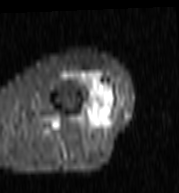
MRI of an extremity soft-tissue mass, one axial slice; position 30 of 103 along the scan axis; STIR; MR volume resampled by the dataset authors to the PET/CT grid (not the native acquisition matrix); 179 × 193 image matrix, field of view 175 × 188 mm. Female patient. Case-level facts recorded for this patient, not image findings: histological type: undifferentiated – high grade; grade: high; site of the primary tumour: left thigh.
Structures marked on this image (expert contour drawn on MRI and transferred to this co-registered scan by the dataset authors):
- gross tumour volume including surrounding oedema: bounding box (x1, y1, x2, y2) in pixels: (64, 73, 117, 116)